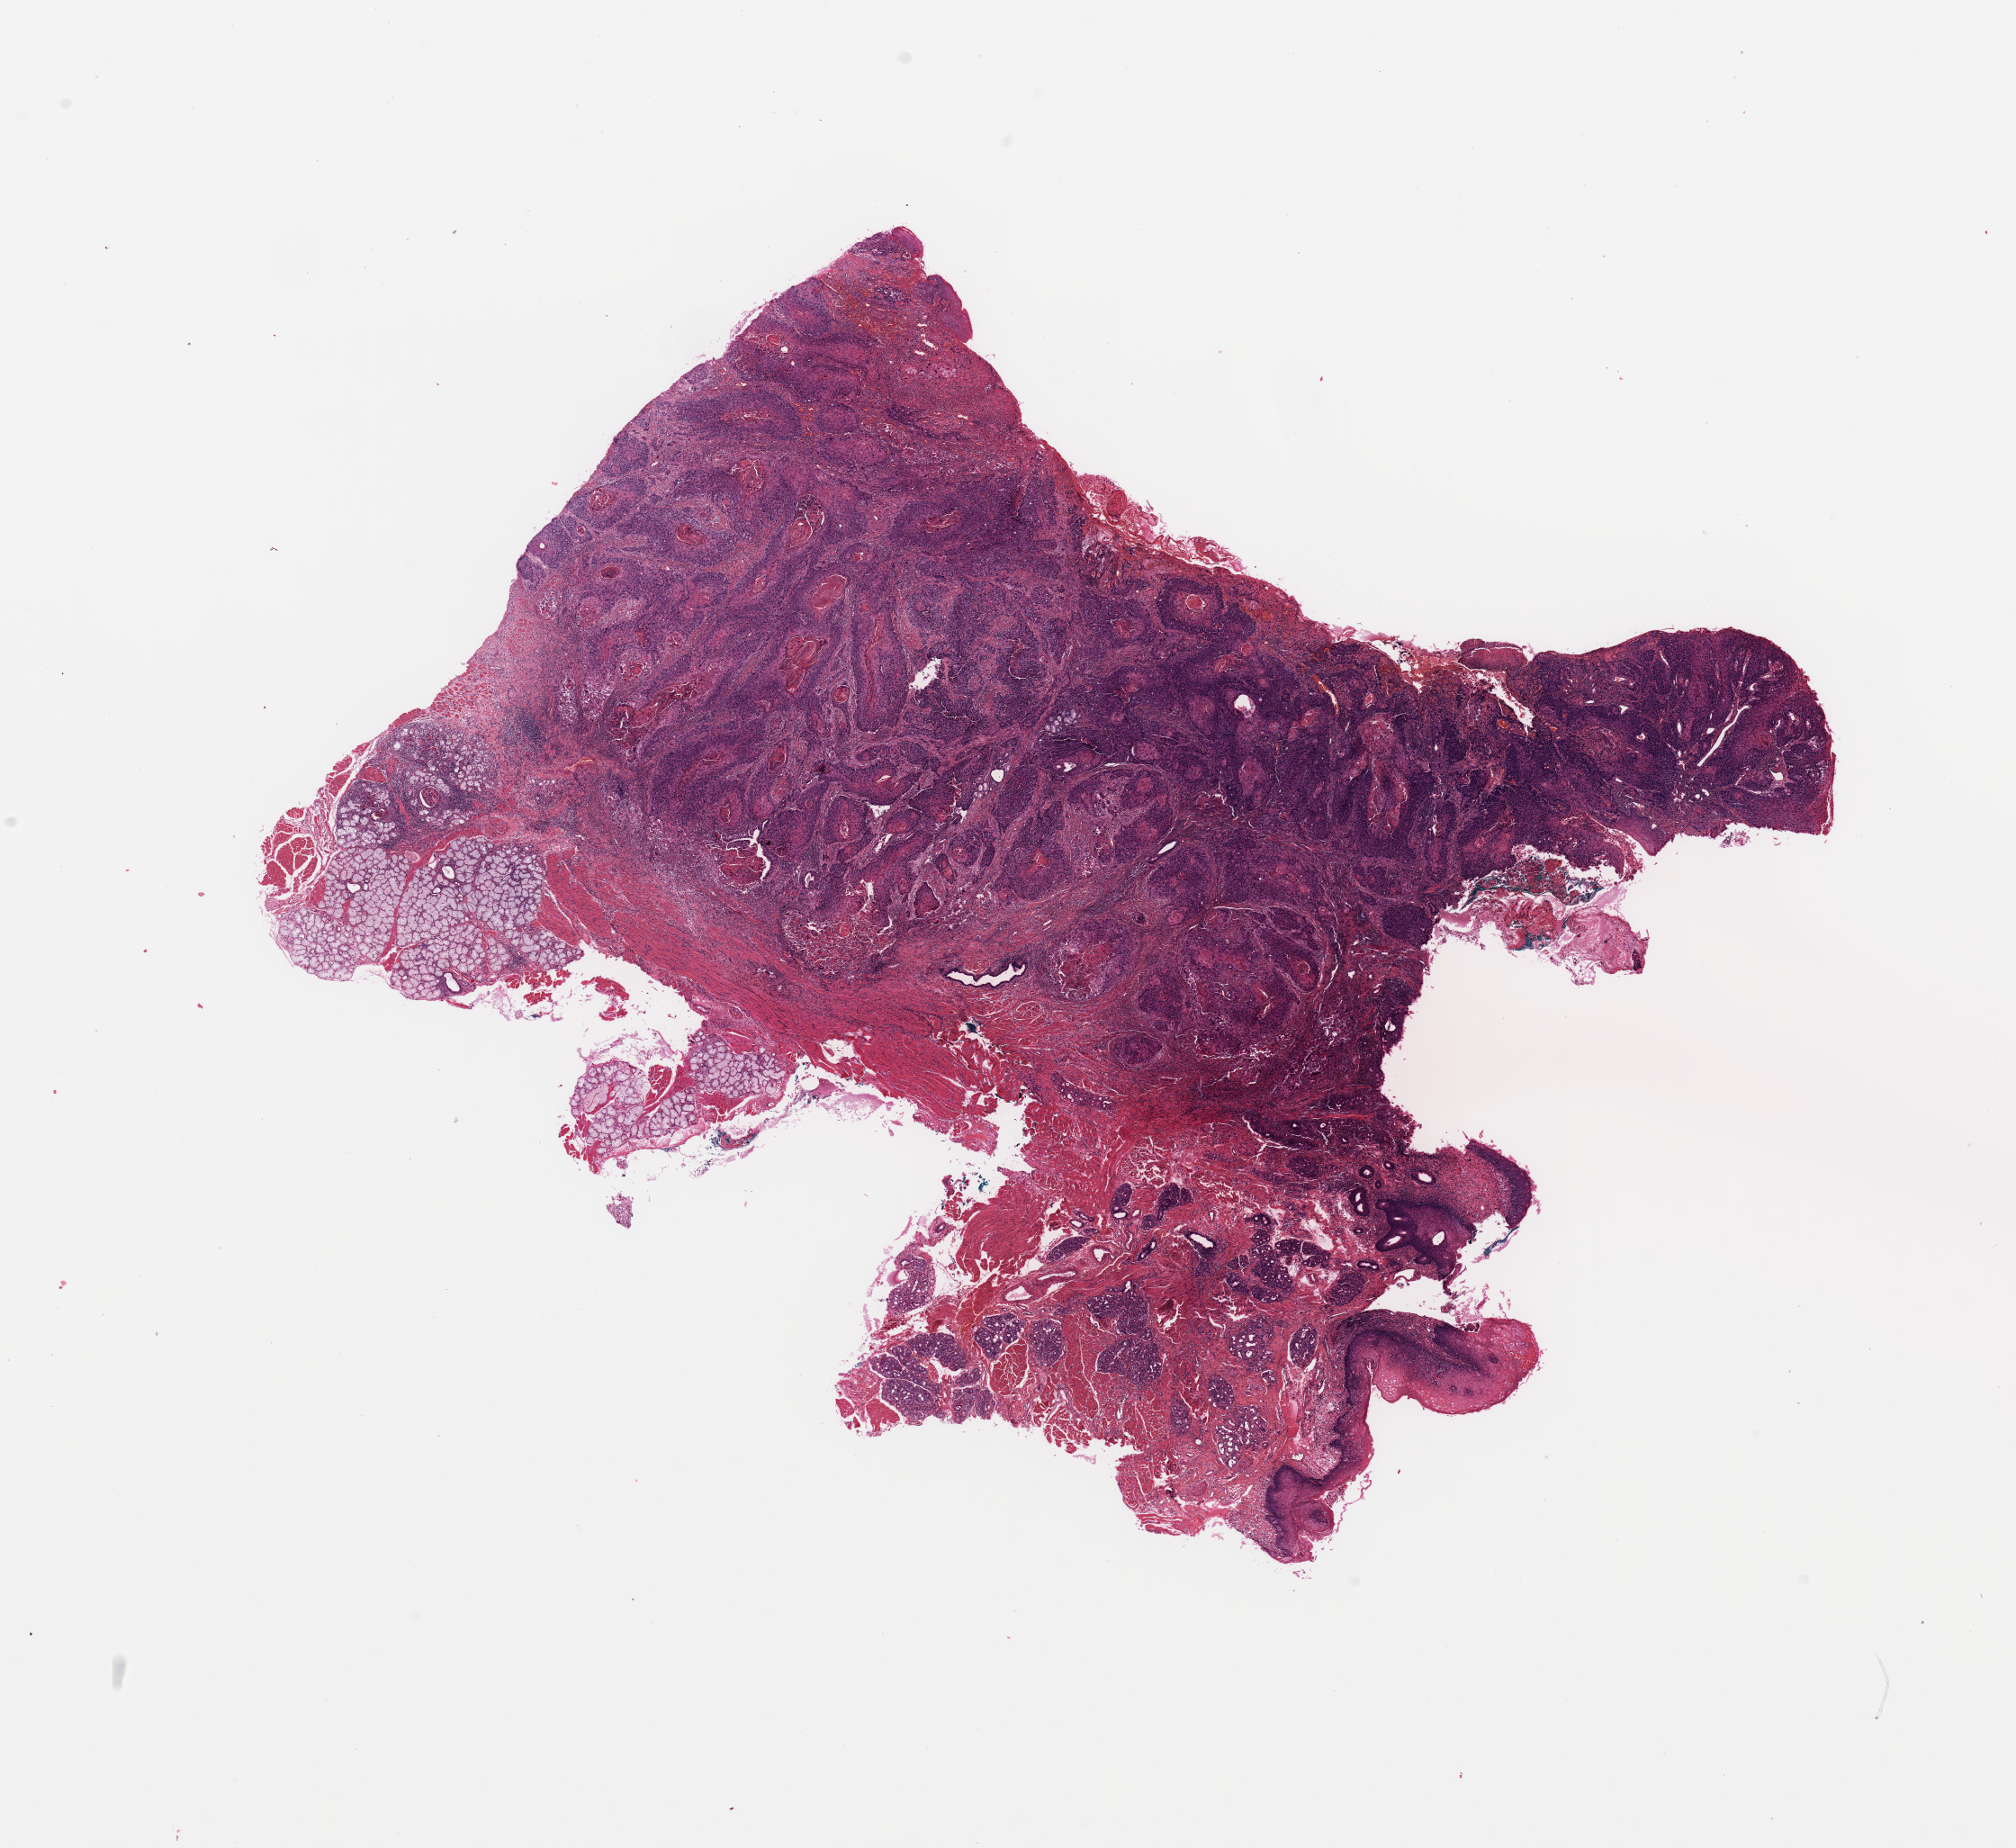
Whole-slide histology image, Hematoxylin and eosin (H&E) stained, a low-resolution overview of the entire scanned area, about 17.7 x 16.2 mm (slide scanned at 20x), tumour tissue sample, sampled site: oropharynx. Patient: male, age 47 years.
Histologic diagnosis: Squamous cell carcinoma, NOS (oropharynx, NOS).